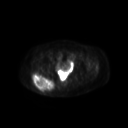
FDG PET of an extremity soft-tissue mass (from a PET/CT study), one axial slice; slice 53 of 267 in the series (ordered by position); 128 × 128 image matrix. Female patient, age 60 years. Case-level facts recorded for this patient, not image findings: histological type: spindle cell suggestive of myxofibrosarcoma; grade: intermediate; site of the primary tumour: right buttock.
Outlined on this slice (expert contour drawn on MRI and transferred to this co-registered scan by the dataset authors):
- gross tumour volume (mass): bounding box <33,73,55,93> (left, top, right, bottom; pixels)